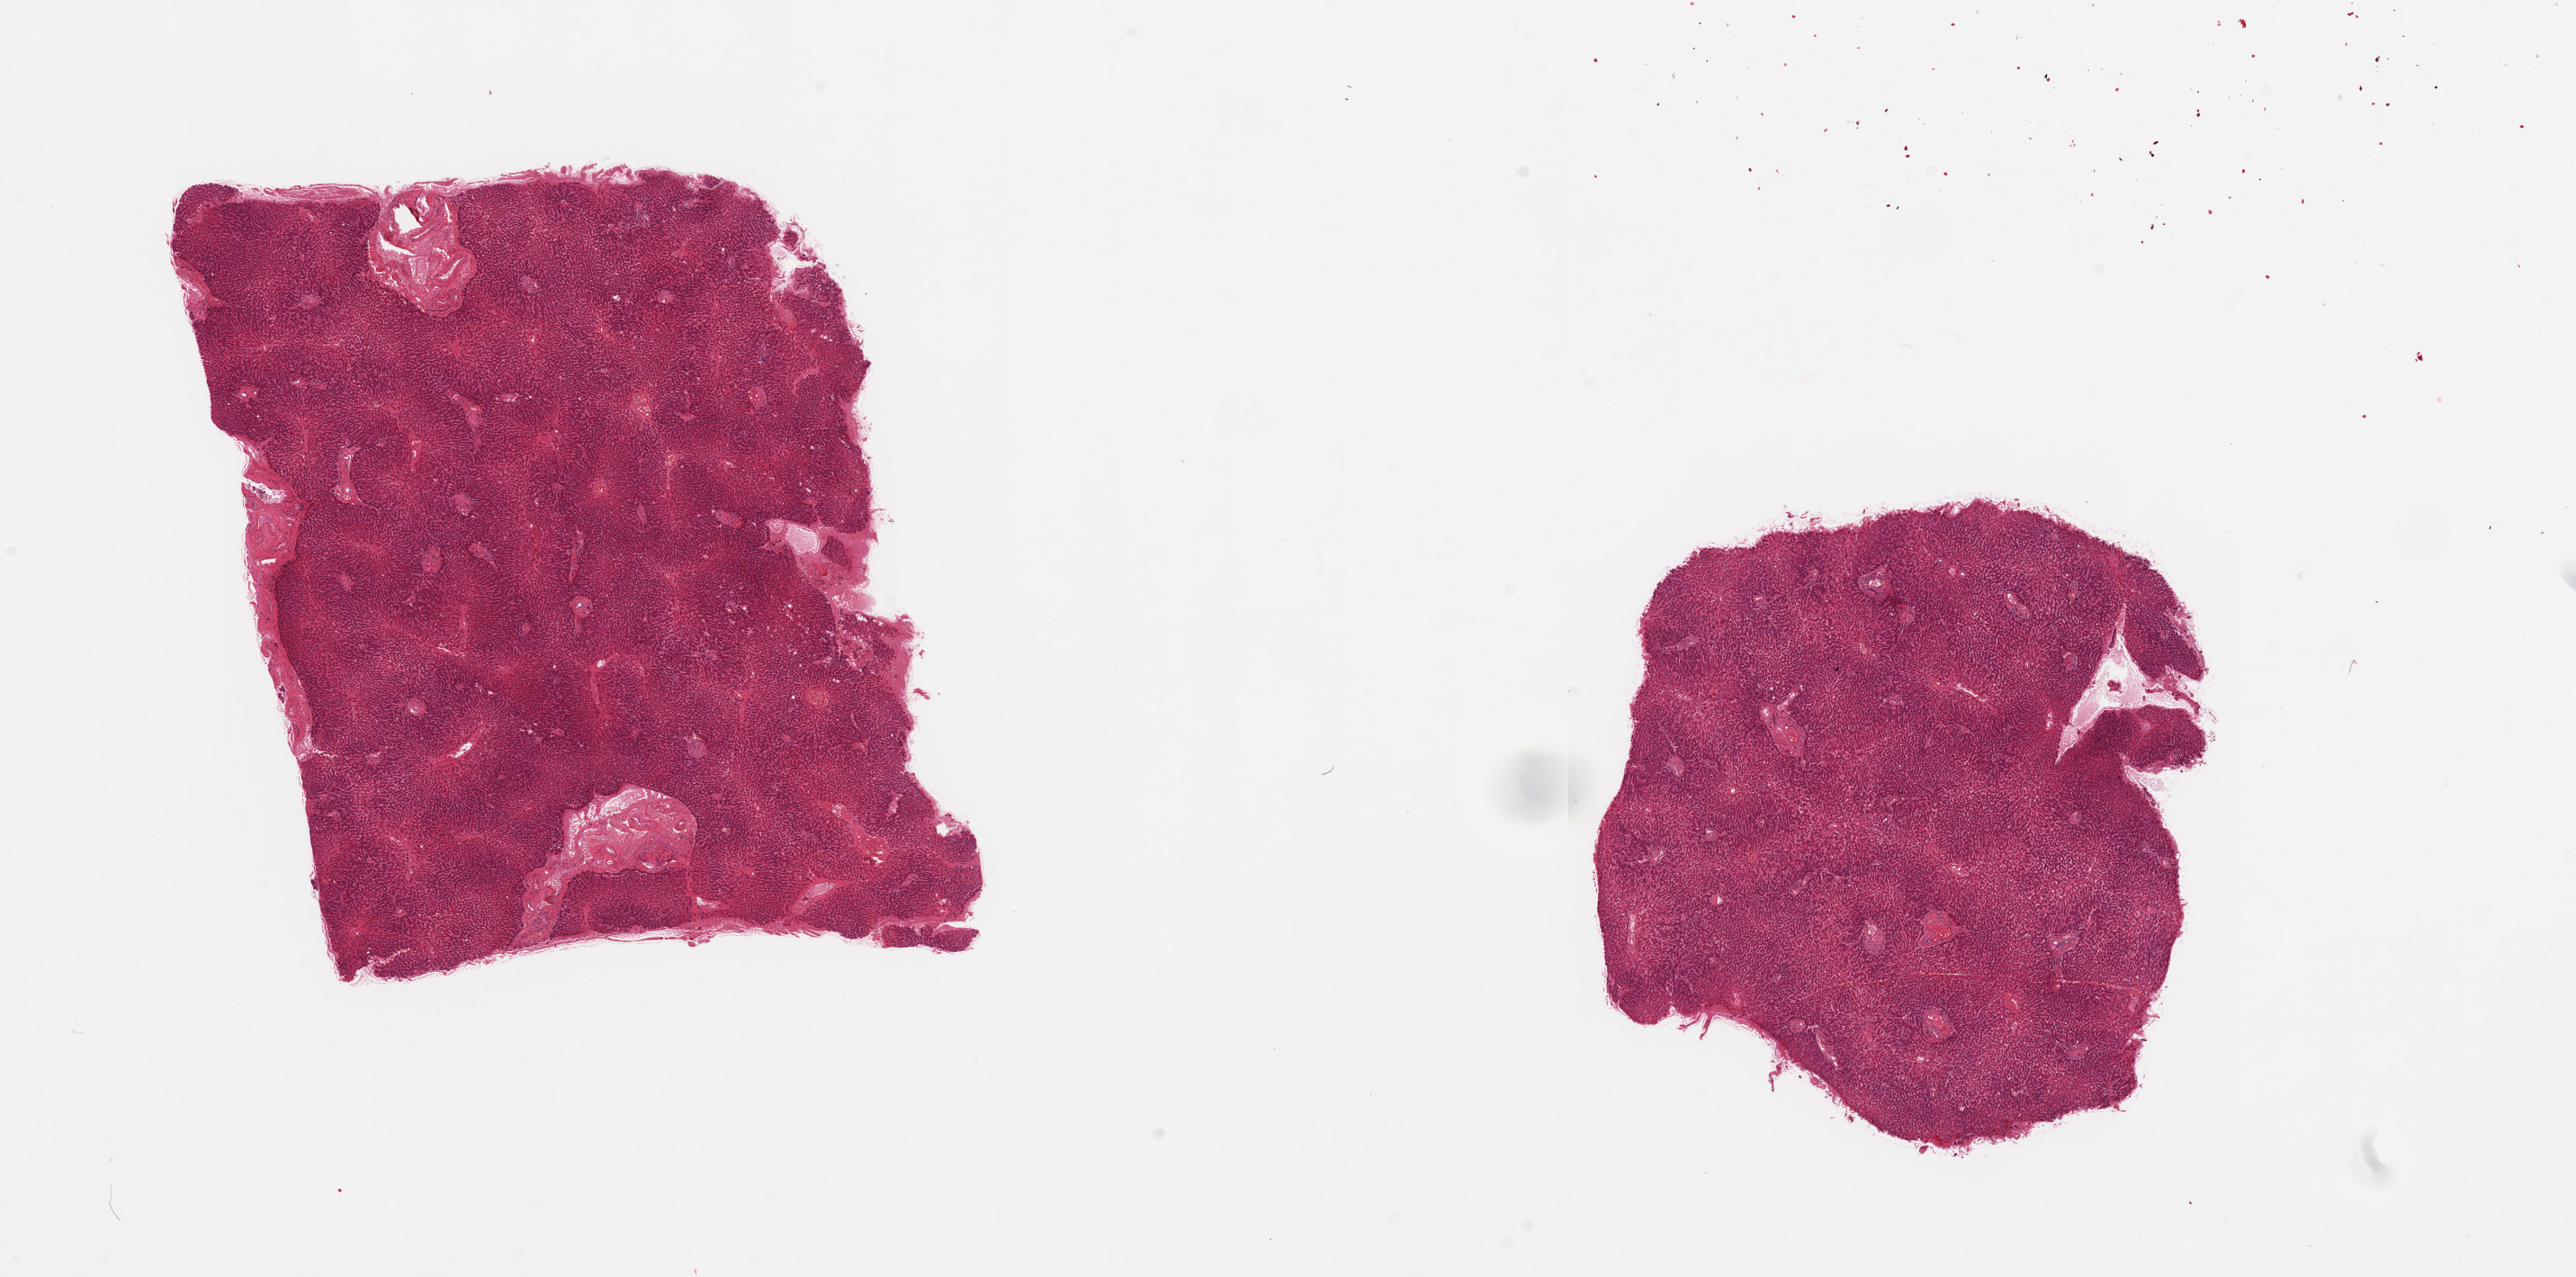
Whole-slide image, haematoxylin and eosin stain — low-resolution overview of the scanned area, about 22.6 x 11.2 mm; PAXgene-fixed paraffin-embedded (PFPE) section; sampled site (target tissue): liver; donor tissue sample. Donor: male.
Reviewer comment on this tissue sample: 2 pieces; congestion and accentuation of portal triads.